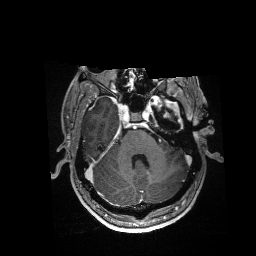
Brain MRI from a brain-tumour surgery series, one axial slice; slice 117 of 176 in the series (ordered by position); T1-weighted post-contrast; 1 mm slice thickness; 256 × 256 image matrix, field of view 256 × 256 mm. Case-level facts recorded for this patient, not image findings: histopathology: Glioblastoma; WHO grade: 4; IDH mutation: no.
Structures marked on this image (outlined manually by an expert reader):
- residual tumour: bounding box (x1, y1, x2, y2) in pixels: (155, 98, 179, 112)